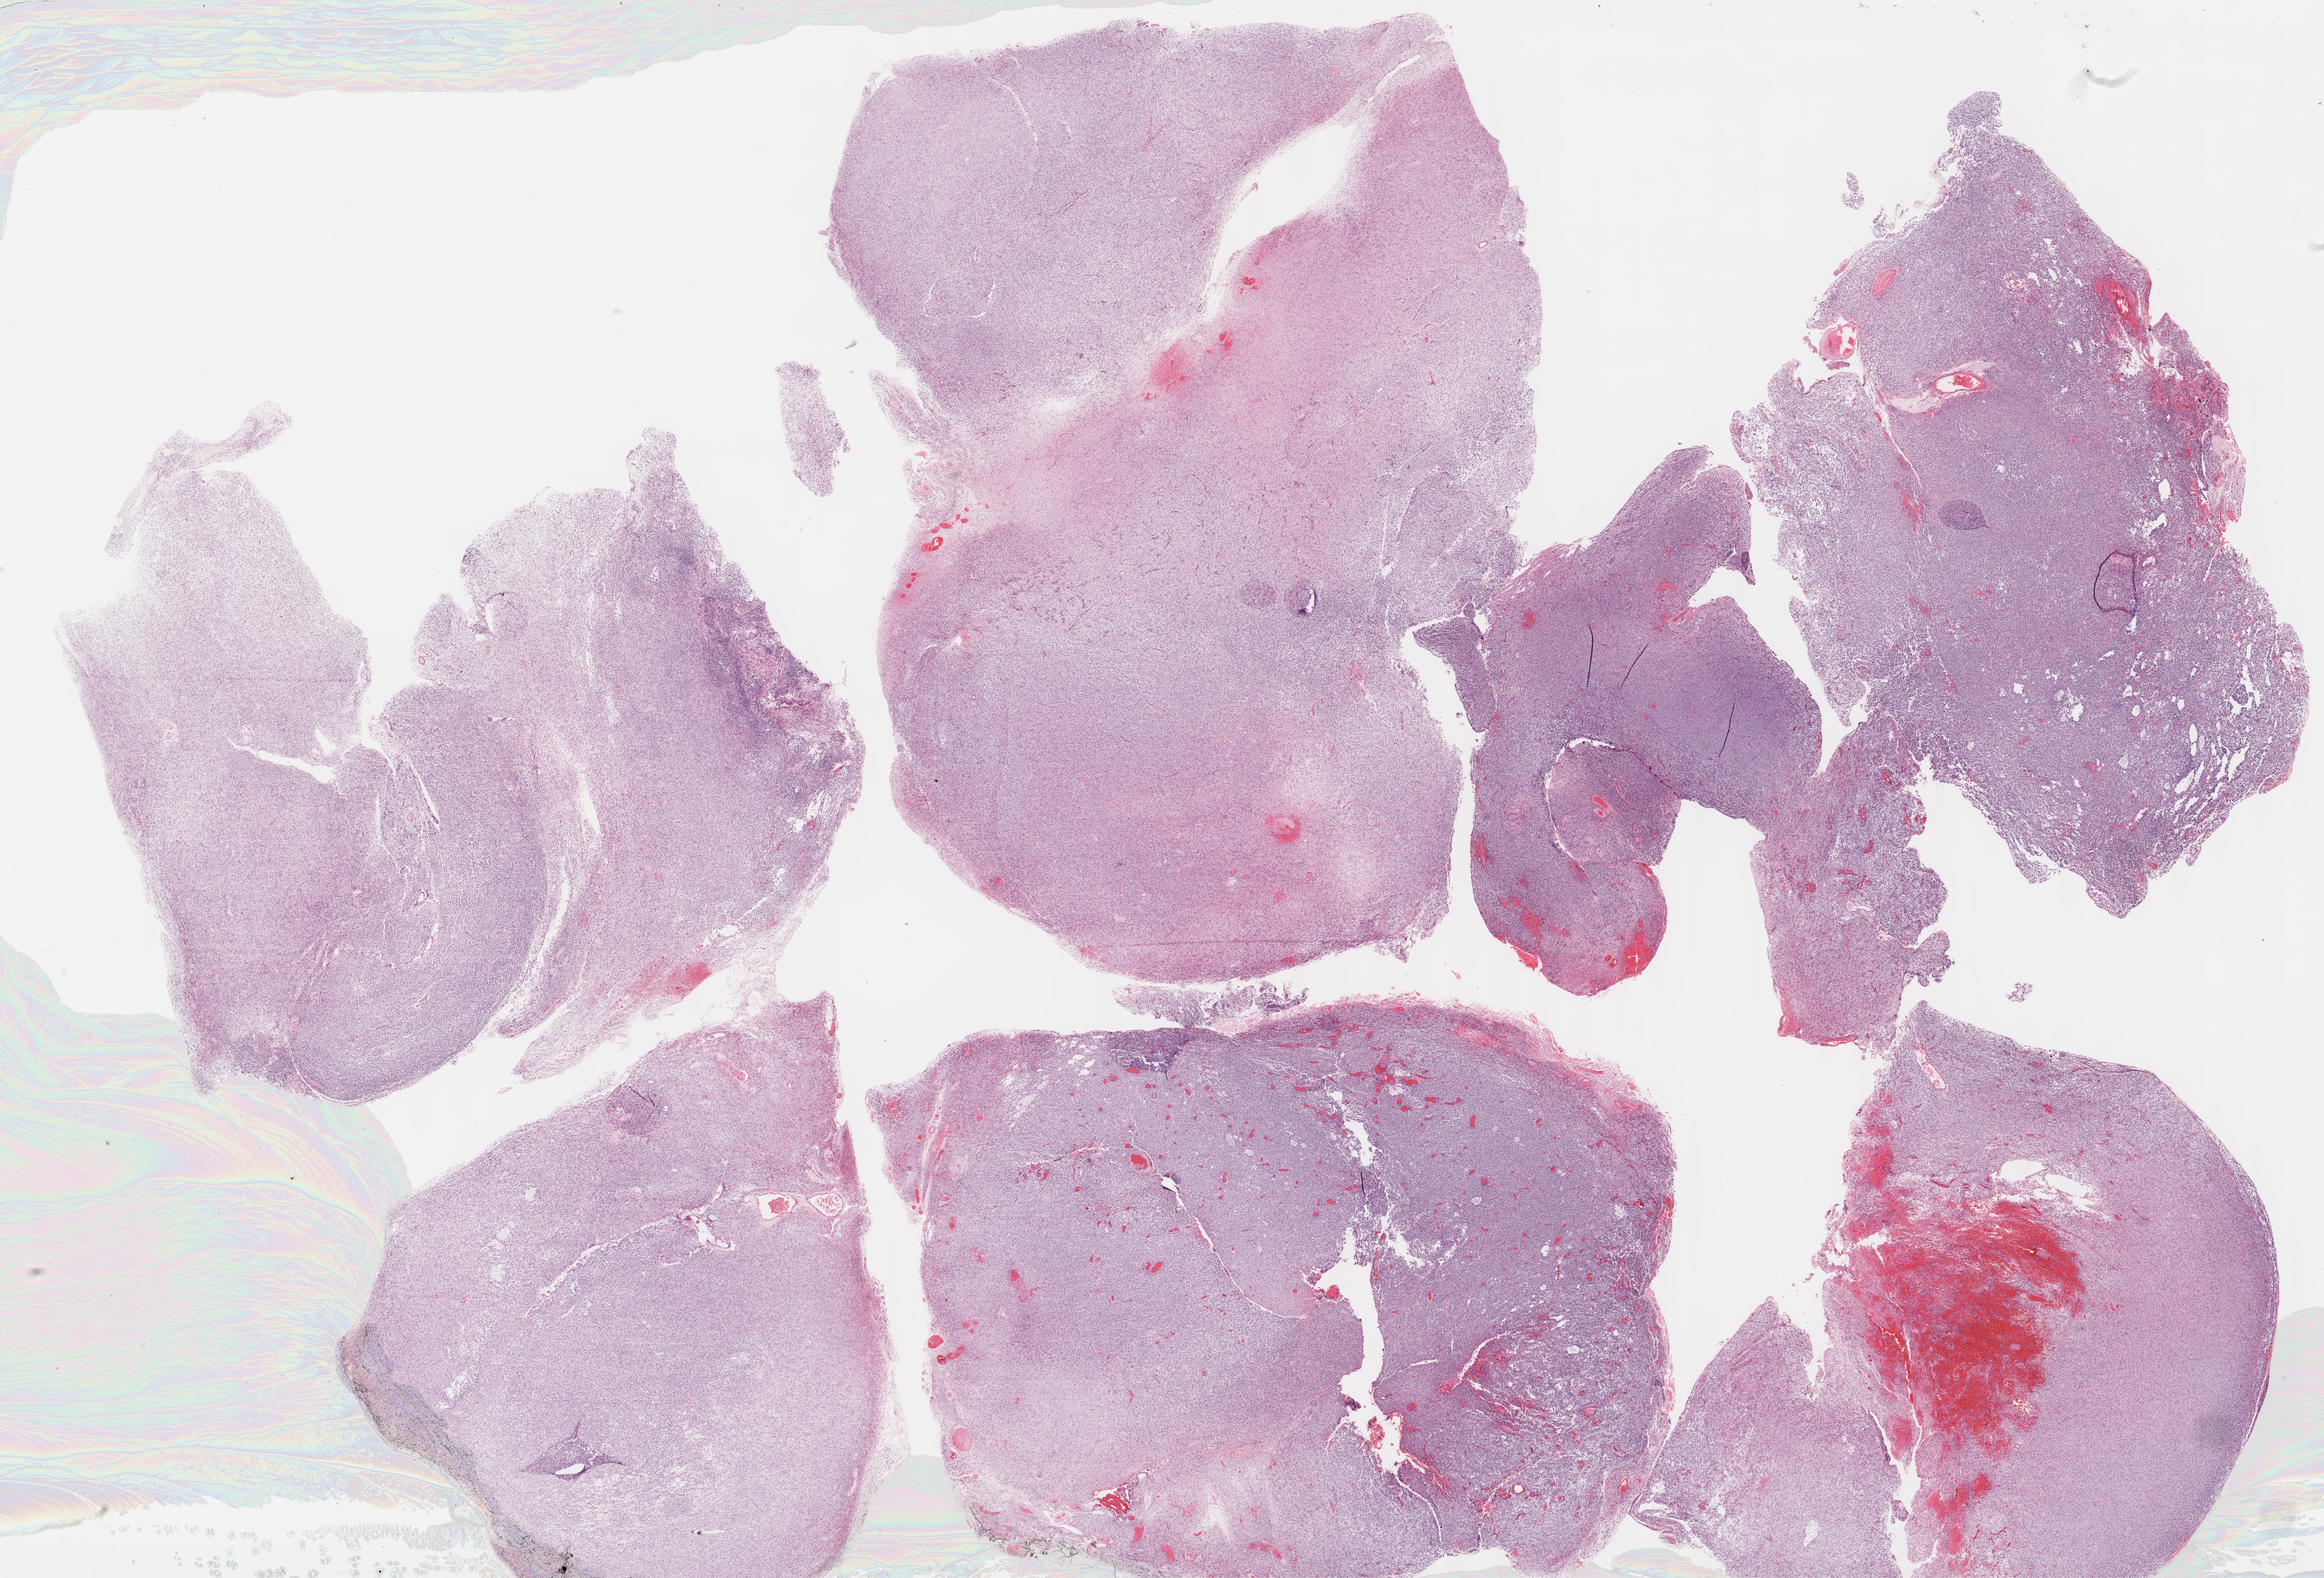
Whole-slide histology image, H&E-stained, low-resolution overview of the scanned area, about 29.2 x 19.8 mm (acquisition: 40x scan). Formalin-fixed paraffin-embedded (FFPE) diagnostic section. Primary tumour sample from the brain. Patient: male, age at initial diagnosis 71 years.
Pathologic diagnosis: Glioblastoma.